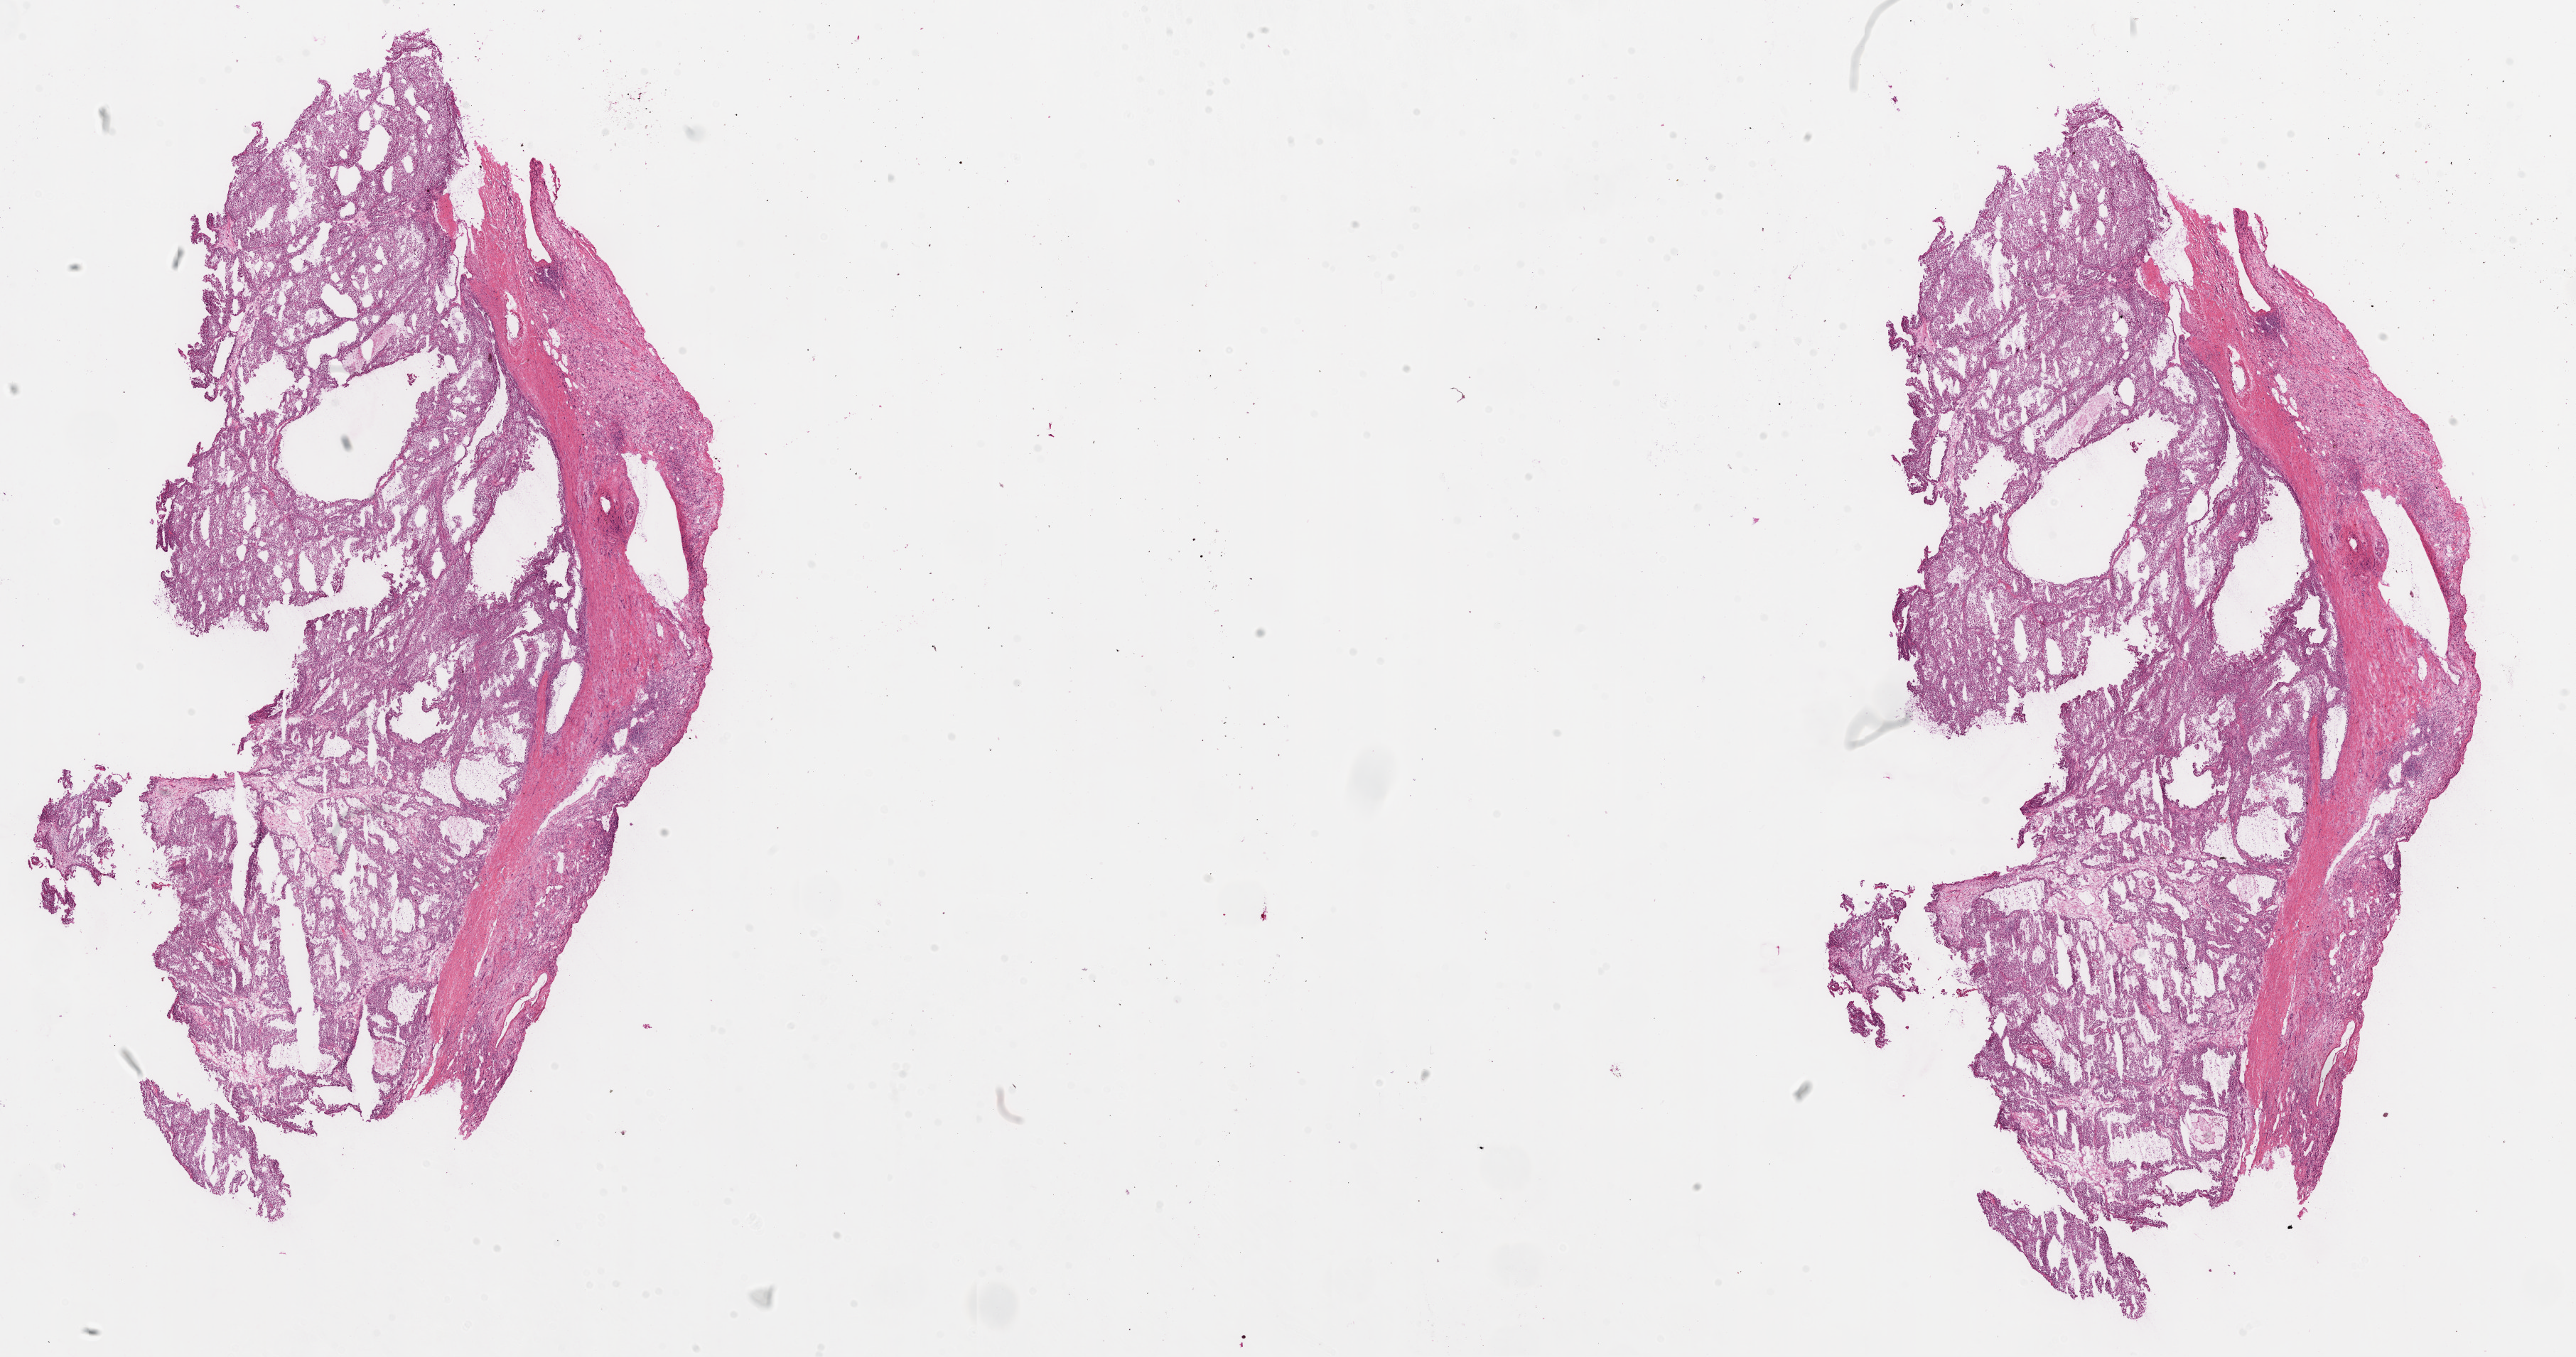
Hematoxylin and eosin (H&E) stained whole-slide image, low-resolution overview of the scanned area, about 29.1 x 15.3 mm (acquisition: 20x scan), frozen section from the top of the tissue portion, primary tumour sample from the kidney. Male, age 41 years at initial diagnosis. Histologic grade: G2 (moderately differentiated). Pathologist review of this section (percent, as recorded): tumour cells 80%, tumour nuclei 75%, normal cells 0%, stromal cells 20%, necrosis 0%.
- AJCC pathologic stage: I
- laterality: right
- pathologic diagnosis: Clear cell adenocarcinoma, NOS
- TNM: T1a NX M0